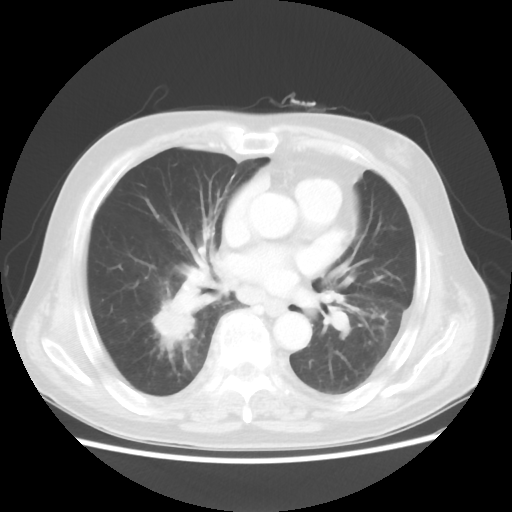
Chest CT, one axial slice; slice 18 of 44 in the series (ordered by position); 100 kVp; lung window (W 1500 / L -600 HU); 5 mm slice thickness; 512 × 512 image matrix. Male patient, age 83 years. Case-level facts recorded for this patient, not image findings: clinical TNM (as recorded): T2 N3 M0.
Annotated regions visible in this slice (bounding box drawn by a radiologist):
- lung tumour (recorded histology: adenocarcinoma): box from (x=144, y=288) to (x=204, y=354) px